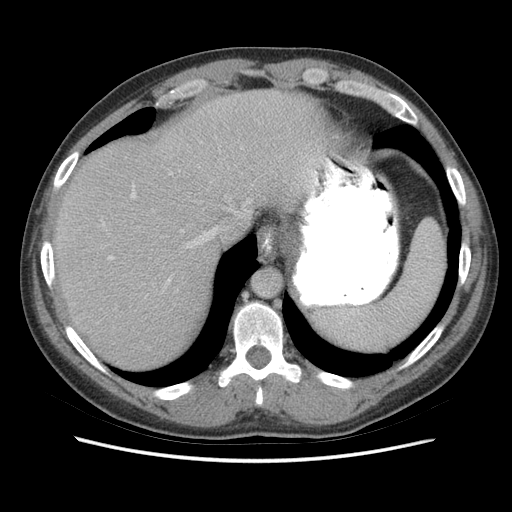
Contrast-enhanced abdominal CT (liver protocol), one axial slice. Position 58 of 73 along the scan axis. Reconstruction kernel STANDARD. 140 kVp. Soft-tissue window (W 400 / L 40 HU). 512 × 512 image matrix, field of view 360 × 360 mm. From the clinical record (not read from this slice): diagnosis: hepatocellular carcinoma (patient treated with transarterial chemoembolisation; whether this scan precedes or follows treatment is not stated here); TNM stage (as recorded): Stage-IIIA; Child-Pugh class: A.
Outlined on this slice (semi-automatically segmented with operator editing):
- abdominal aorta: bounding box <253,269,282,296> (left, top, right, bottom; pixels)
- liver parenchyma outside the tumour (the mass and vessels are separate outlines, so this box may not span the whole liver): <52,90,326,368>
- liver vessels: <108,159,318,281>